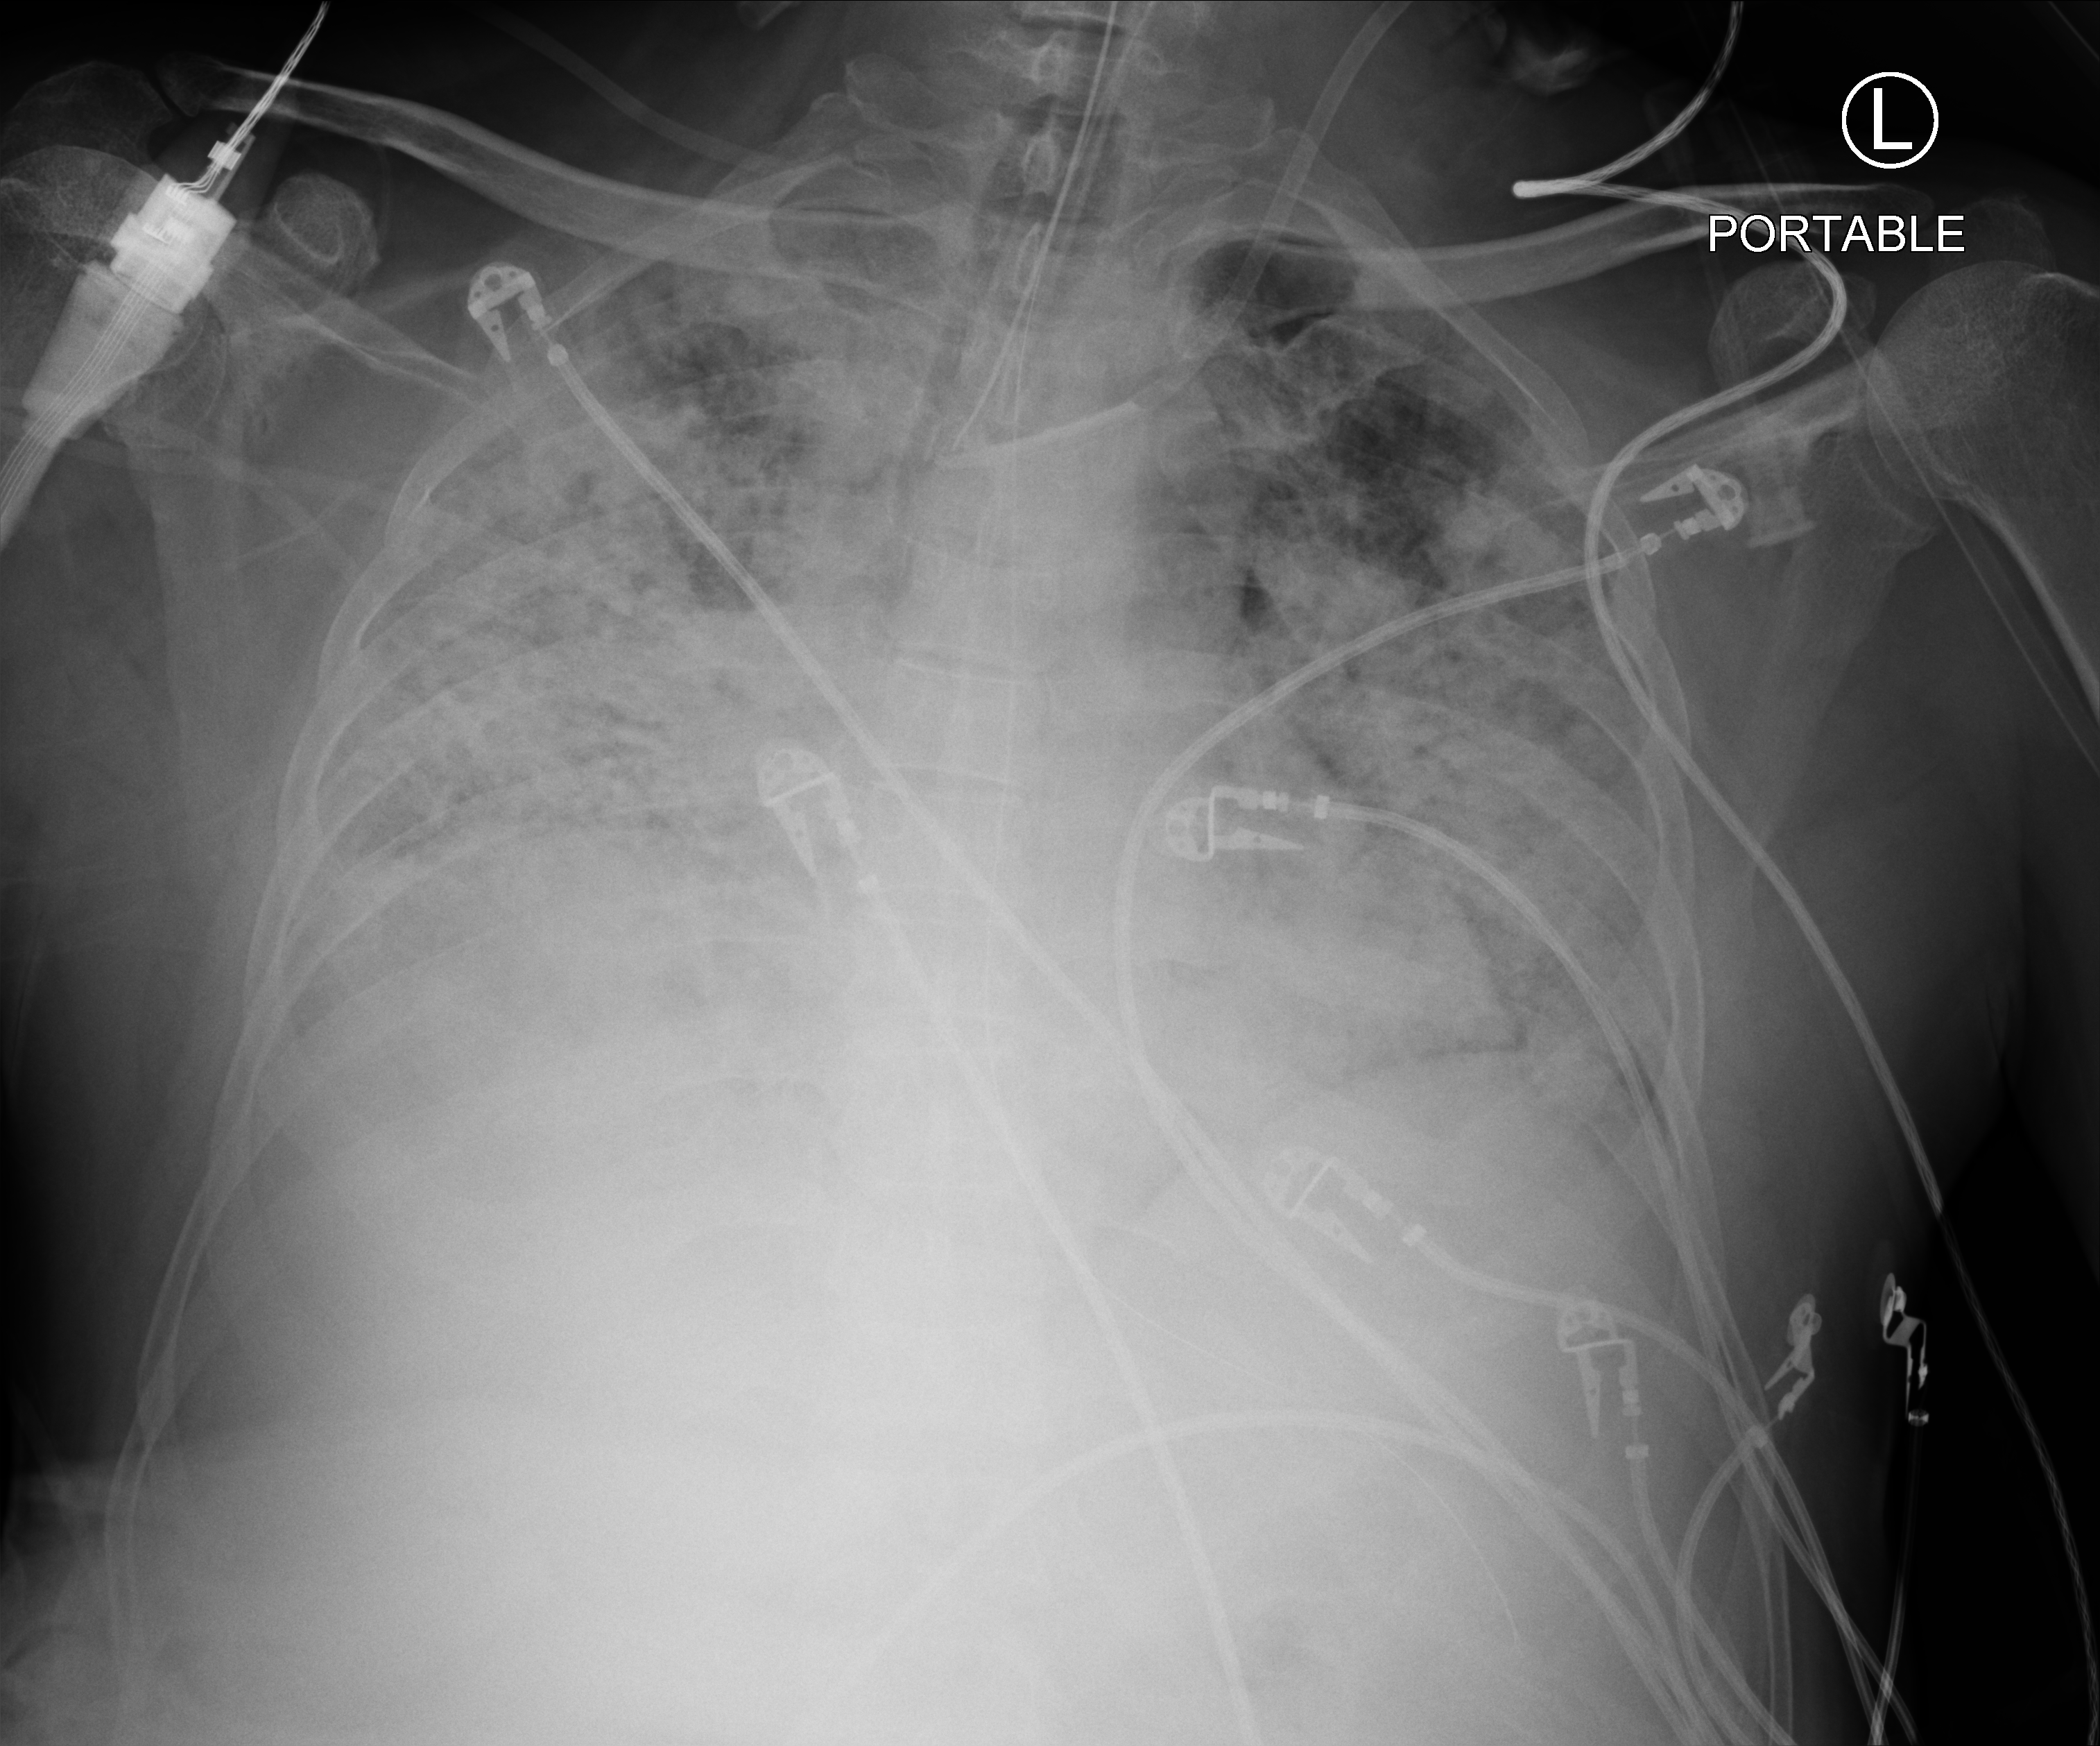
Bedside chest radiograph (computed radiography); anteroposterior (AP) projection. Male patient hospitalised with COVID-19, age 60–74 years.
Admission-level facts for this patient (not findings on this image; timing relative to this image not recorded):
- mechanically ventilated during this hospital stay: yes
- admitted to intensive care during this hospital stay: yes